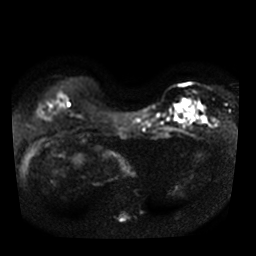
Breast MRI, one axial slice. Diffusion-weighted series; image 2 of 4 stored at this slice position (different b-values; order by instance number). 3 T. 5 mm slice thickness. 256 × 256 image matrix. Female patient.
Outlined on this slice (manually delineated by an expert):
- tumour on diffusion-weighted imaging: bounding box <185,104,201,116> (left, top, right, bottom; pixels)